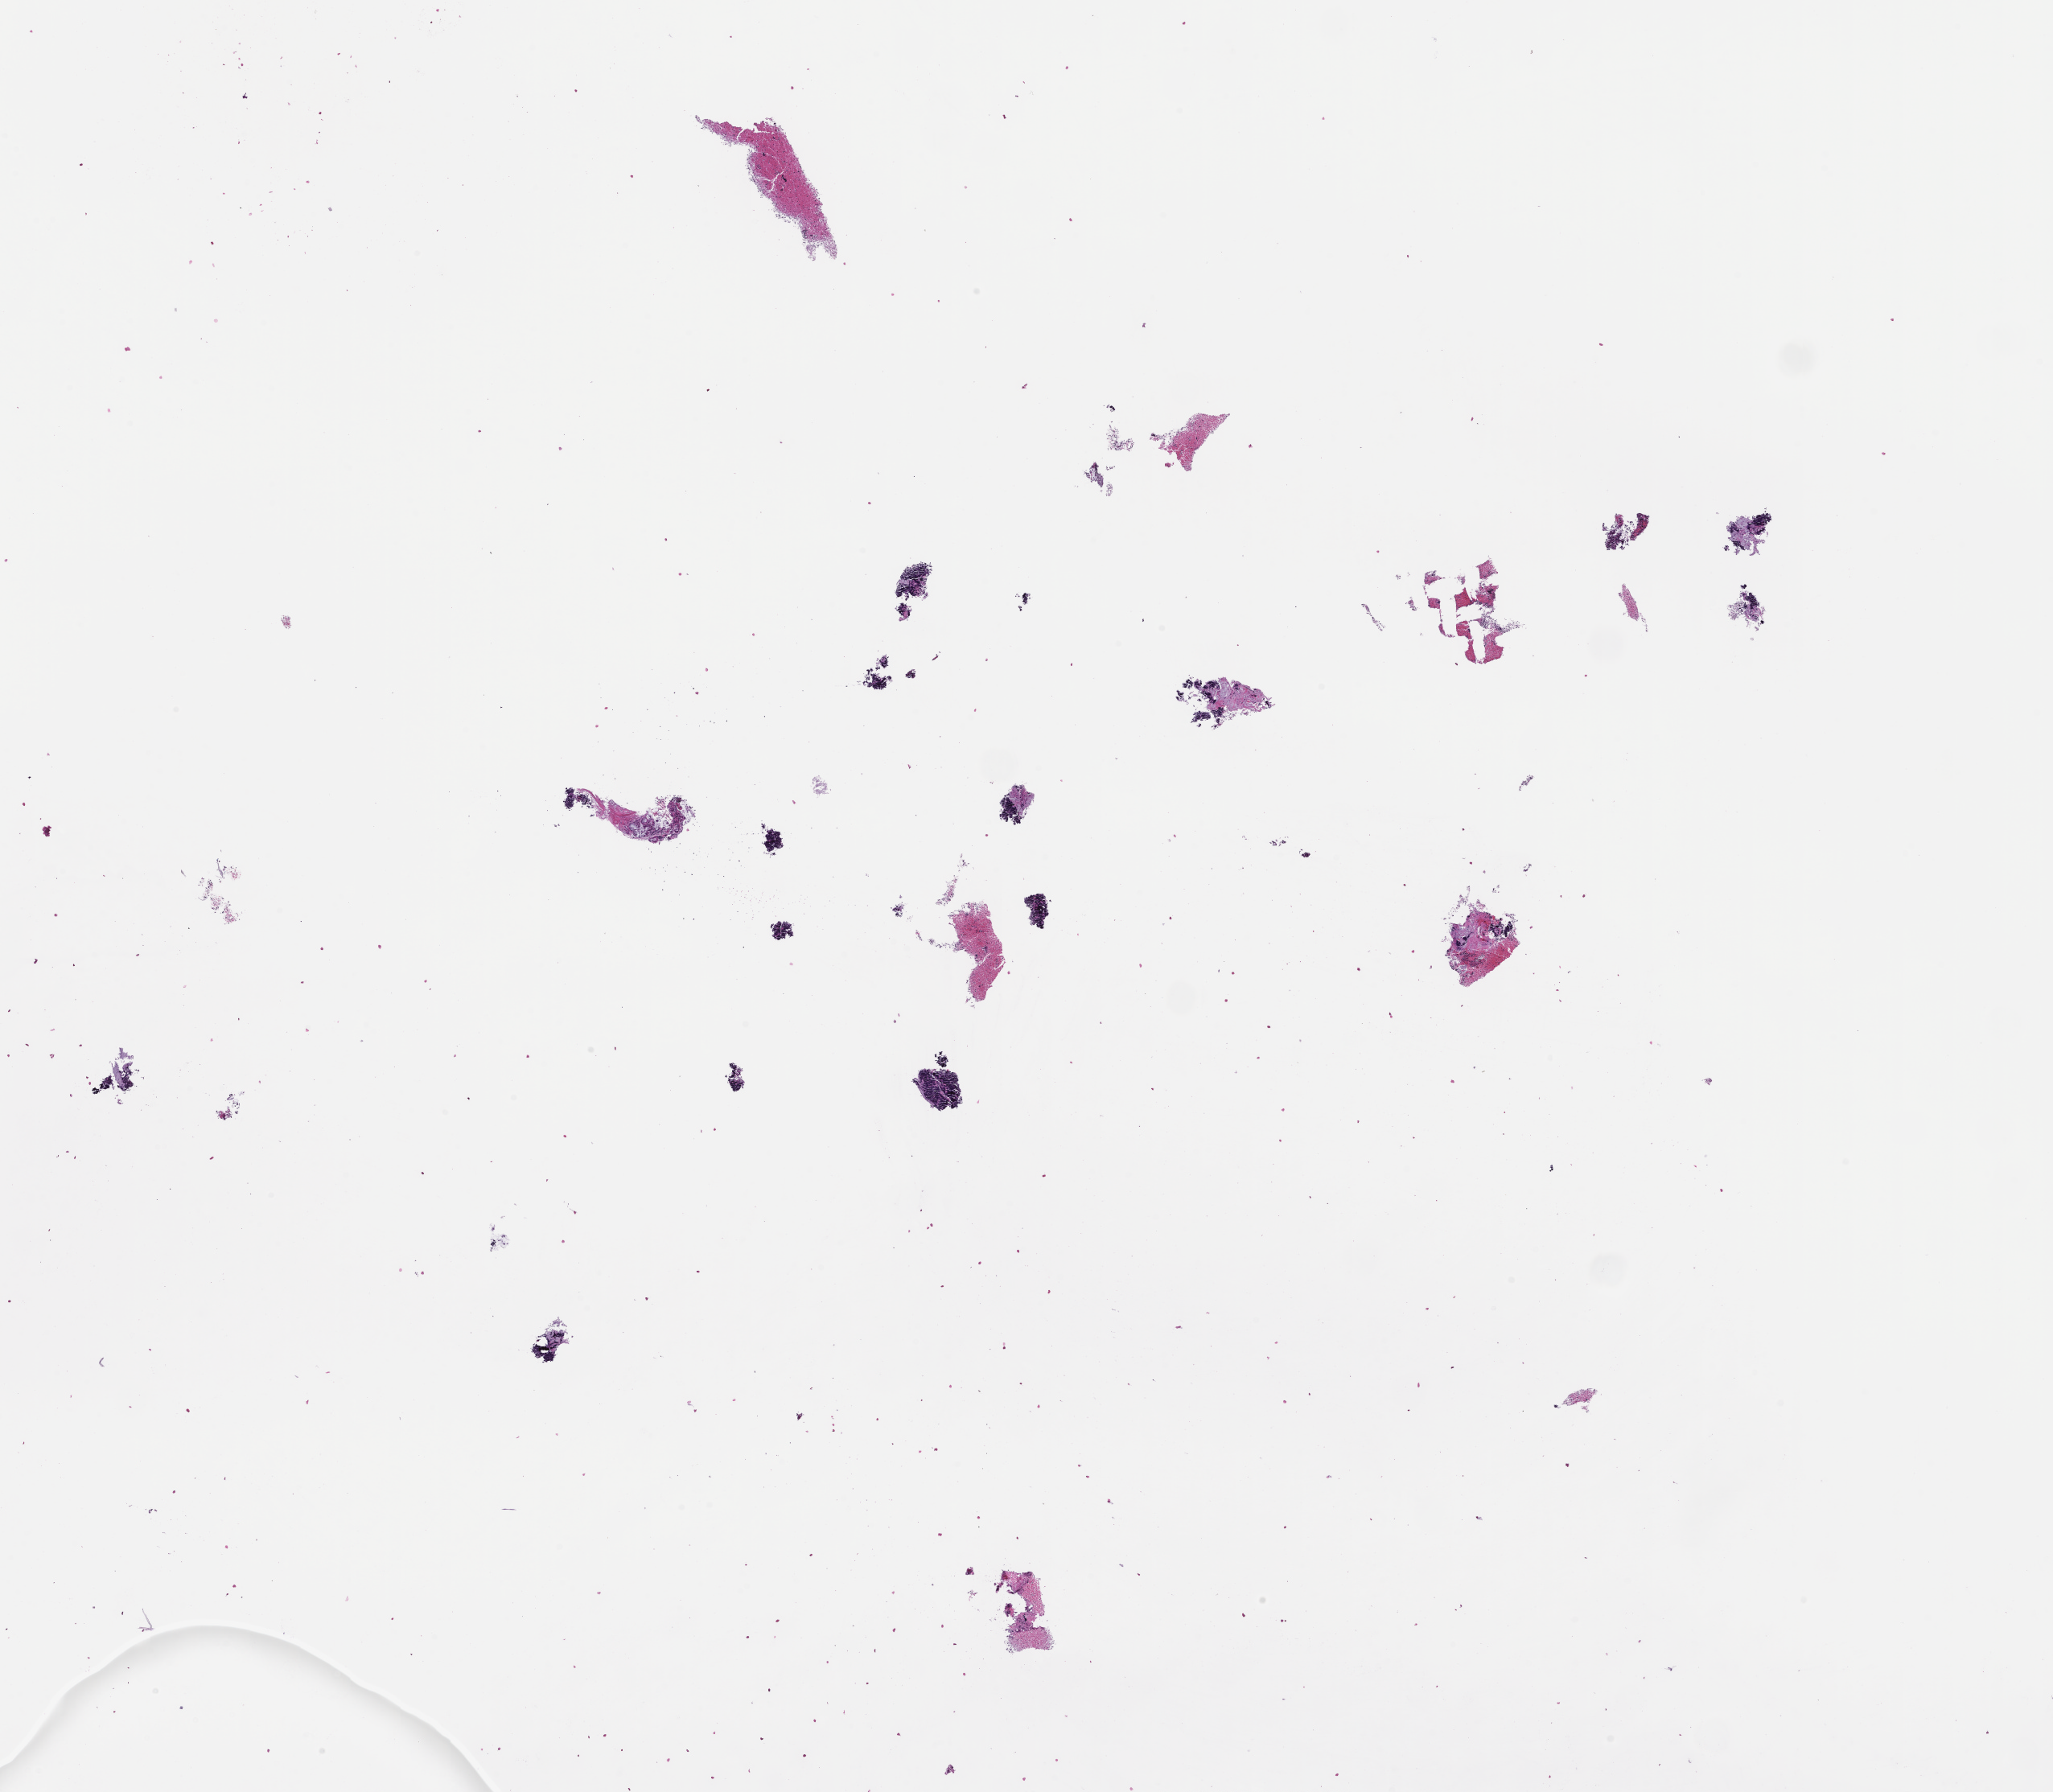
Whole-slide image, H&E stain — low-resolution overview of the scanned area, about 20.6 x 18.0 mm; formalin-fixed, paraffin-embedded (FFPE) tissue; specimen time point: collected at baseline (before treatment). Female patient.
This section: metastatic tumor tissue. Primary diagnosis of the patient: Small Cell Lung Carcinoma.